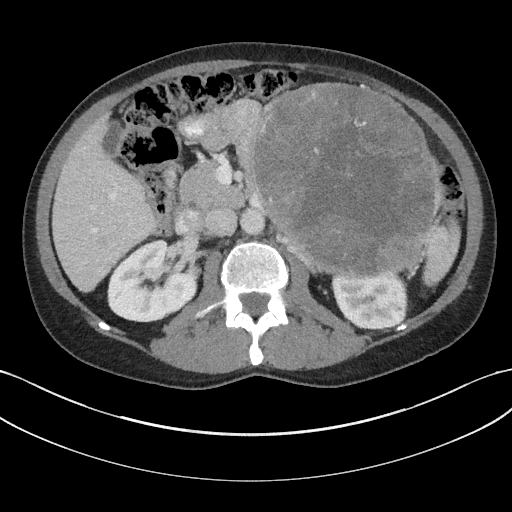
Contrast-enhanced abdominal CT, one axial slice. Slice 99 of 147 in the series (ordered by position). Reconstruction kernel I31f/3. 100 kVp. Intravenous contrast given. Soft-tissue window (W 400 / L 40 HU). 3 mm slice thickness. 512 × 512 image matrix, field of view 384 × 384 mm. Male patient, age 58 years. From the clinical record (not read from this slice): diagnosis: adrenocortical carcinoma; tumour side: left adrenal; tumour size at pathology: 22 cm; Ki-67 index: 26 %; stage (as recorded): 2.
Annotated regions visible in this slice (semi-automatically segmented with operator editing):
- mass: bounding box <254,84,434,276> (left, top, right, bottom; pixels)